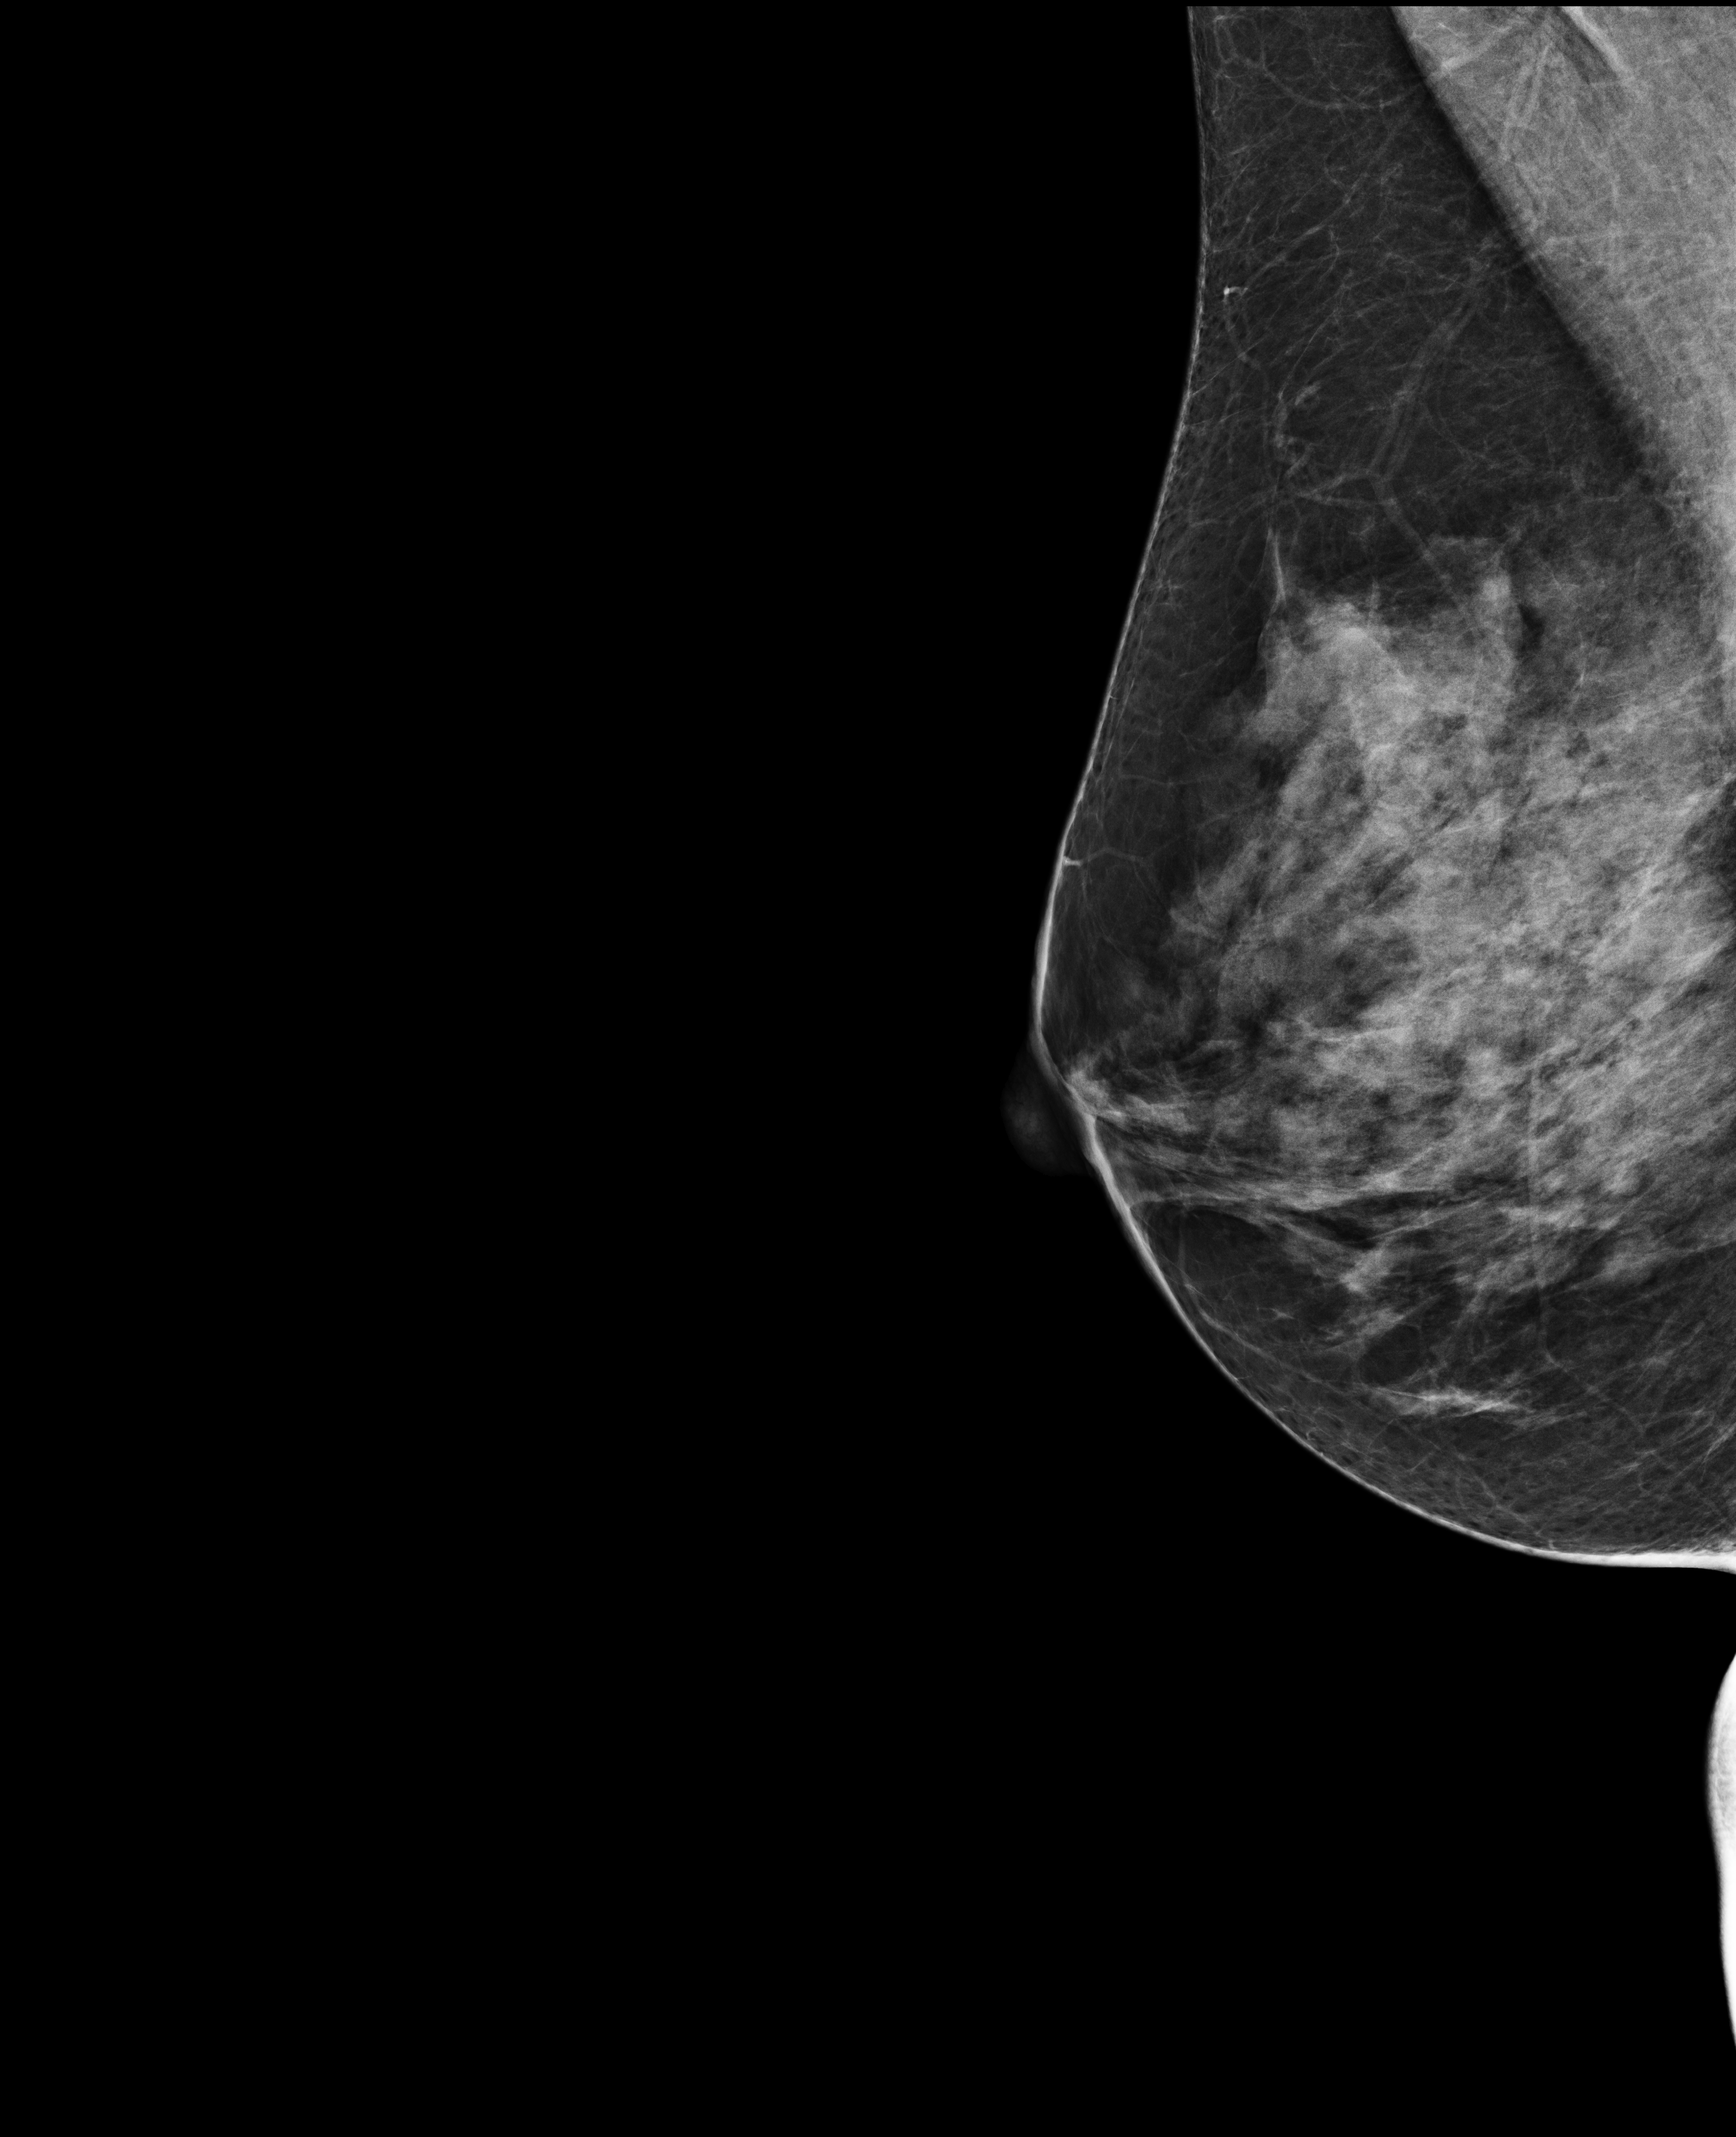
Full-field digital mammogram (FFDM); right breast; mediolateral oblique (MLO) view; annual screening mammography examination; compressed breast thickness 55 mm. Female patient, age 50 years.
Final BI-RADS category for the screening round (tomosynthesis exam, both breasts): category 1.